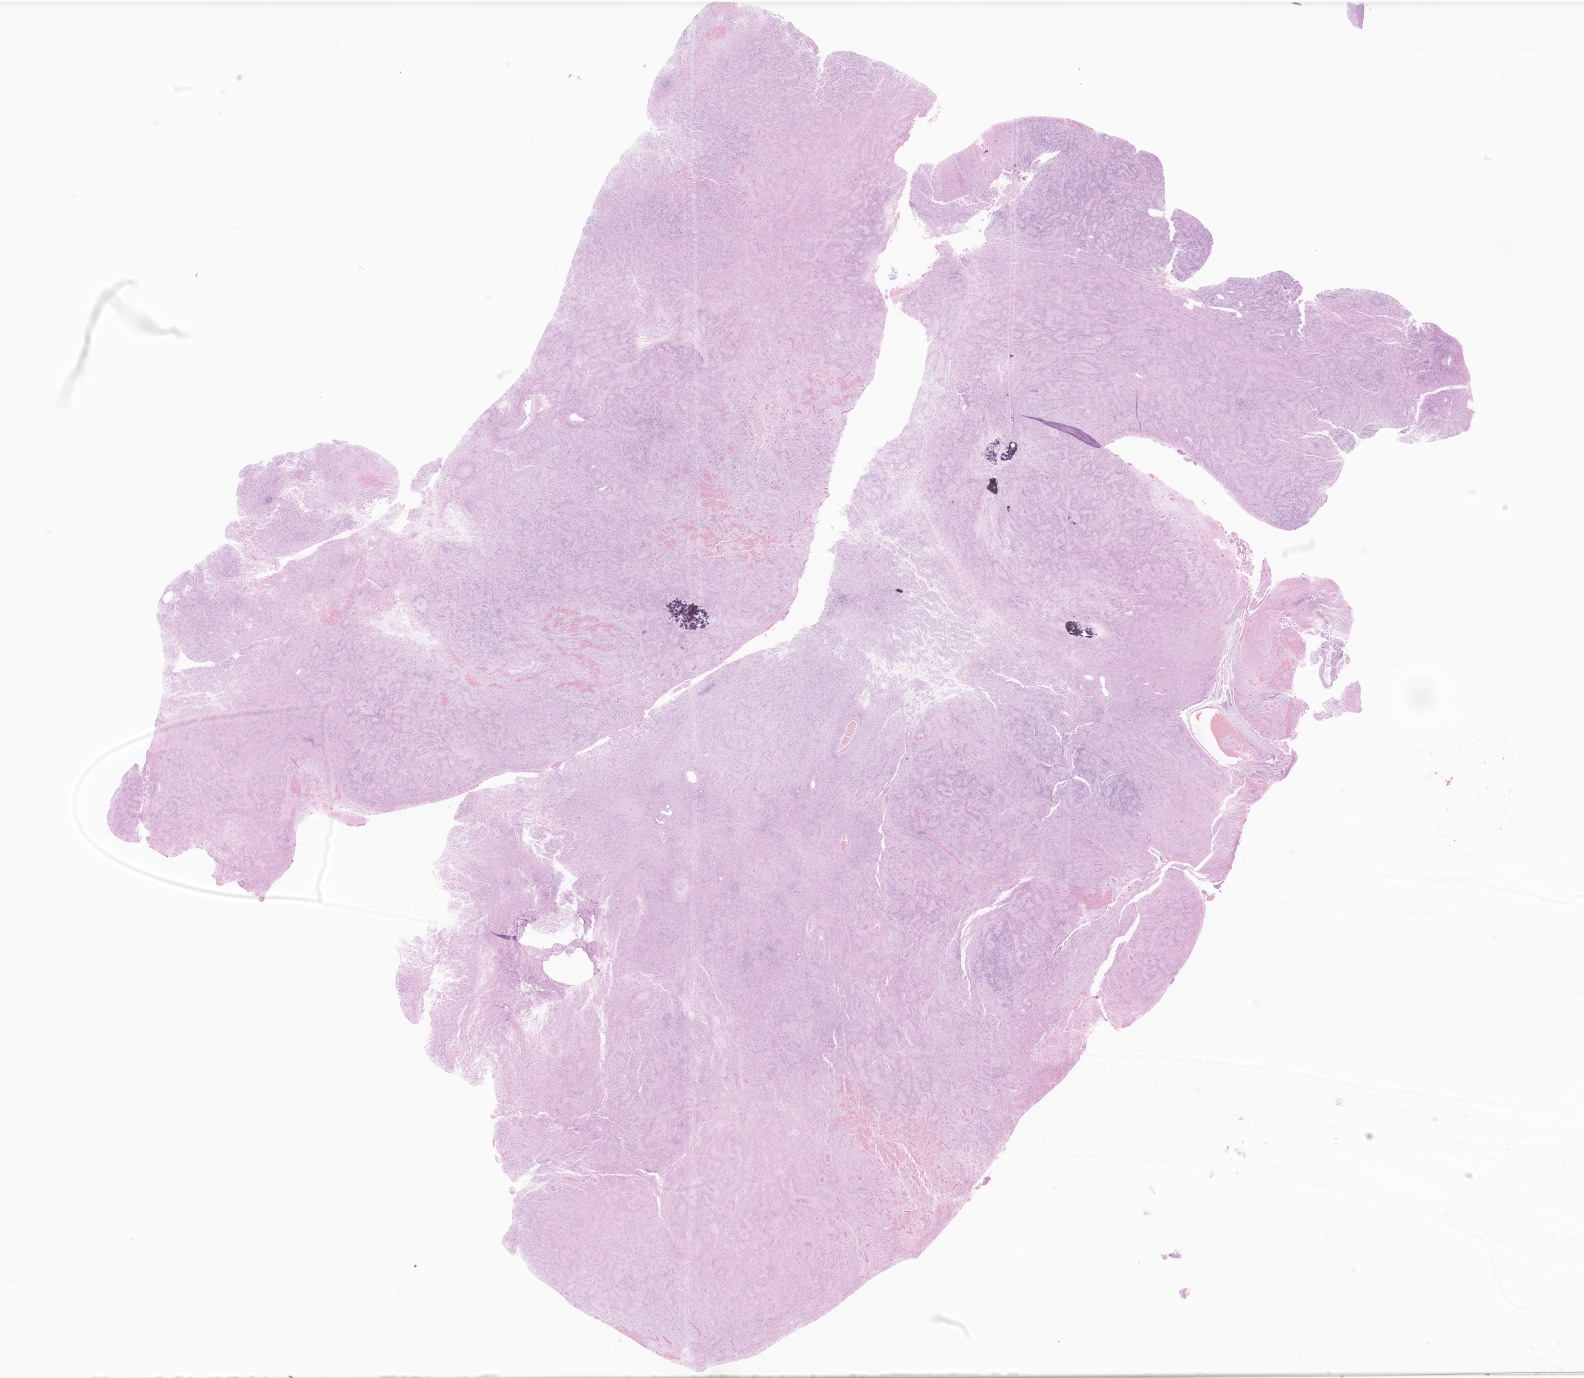
Haematoxylin and eosin whole-slide image of tumor tissue from the brain — shown as a low-resolution overview of the whole scanned area (about 26.7 x 23.2 mm). FFPE section. Male patient, age 53 months (4 years 5 months).
* recorded diagnosis: Ependymoma, NOS